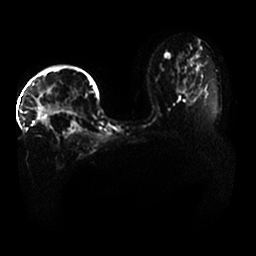
Breast MRI, one axial slice; position 23 of 33 along the scan axis; diffusion-weighted series; image 2 of 4 stored at this slice position (different b-values; order by instance number); 1.5 T; 4 mm slice thickness; 256 × 256 image matrix. Female patient.
Outlined on this slice (manually delineated by an expert):
- tumour on diffusion-weighted imaging: box from (x=39, y=101) to (x=71, y=130) px